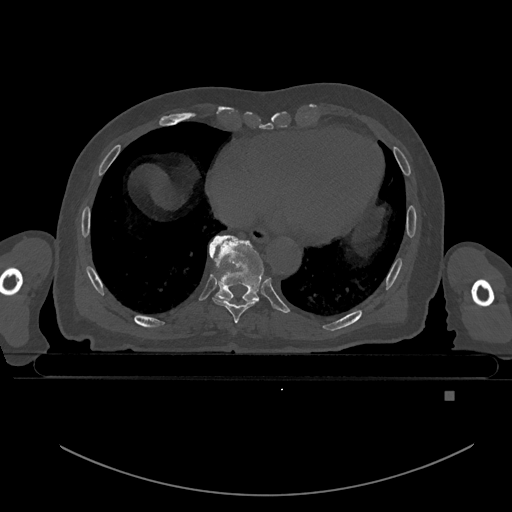
CT including the spine, one axial slice; slice 175 of 969 in the series (ordered by position); bone window (W 1800 / L 400 HU); 512 × 512 image matrix, field of view 456 × 456 mm. Male patient, age 82 years. From the clinical record (not read from this slice): primary cancer: prostate; vertebrae with lytic lesions (as recorded): T11, T9, T8, T2.
Annotated regions visible in this slice (semi-automatically segmented with operator editing):
- T8 vertebra: bounding box <212,297,255,323> (left, top, right, bottom; pixels)
- T9 vertebra: <209,235,264,303>